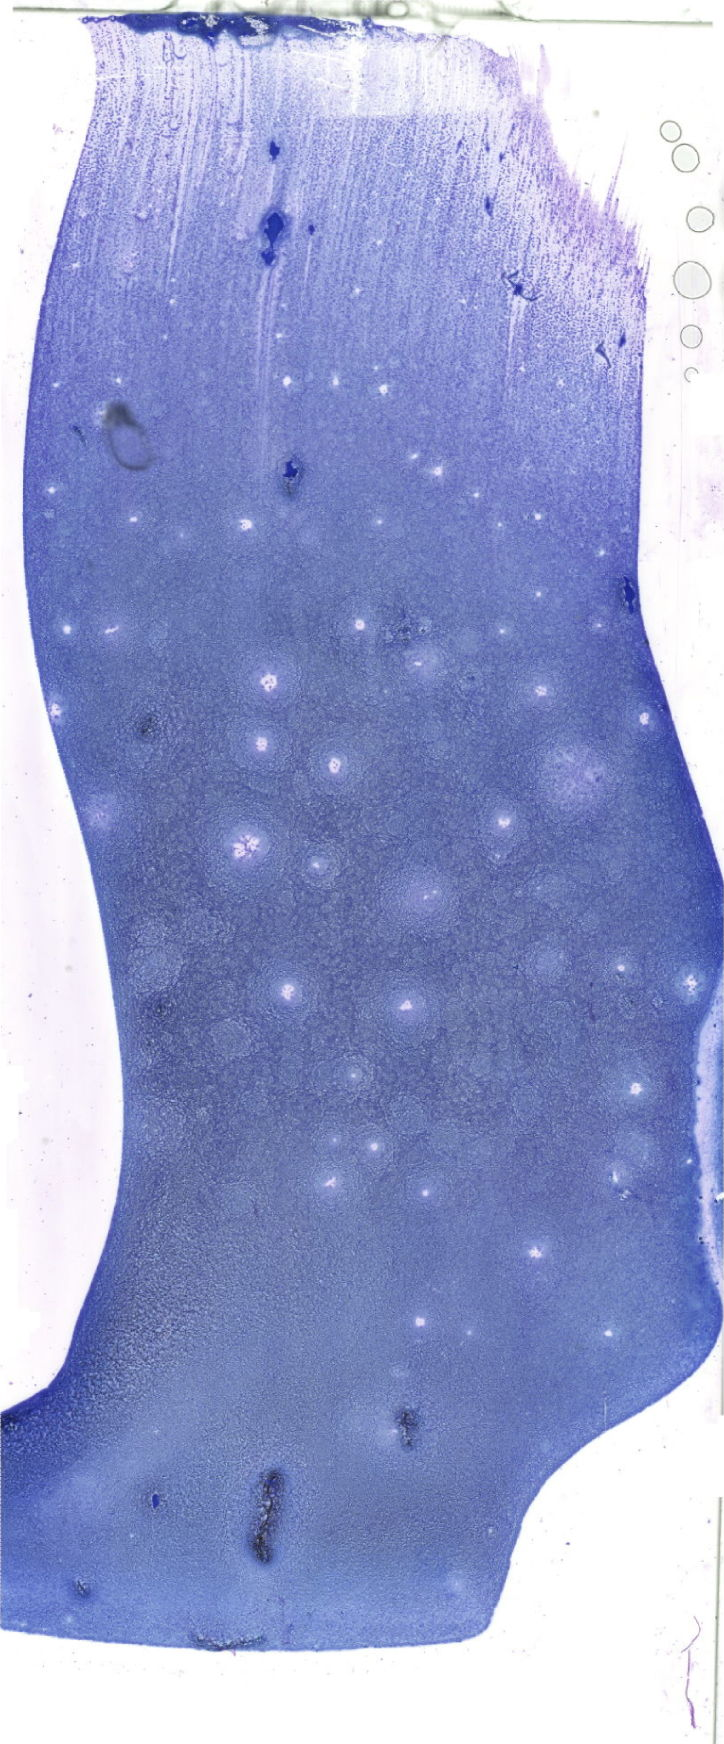
May-Grünwald-Giemsa (MGG)-stained marrow aspirate smear (whole slide) — low-resolution overview of the scanned area, about 20.5 x 49.4 mm. Patient sex: male.
Diagnosis: Acute Myelomonocytic Leukemia with Abnormal Eosinophils.